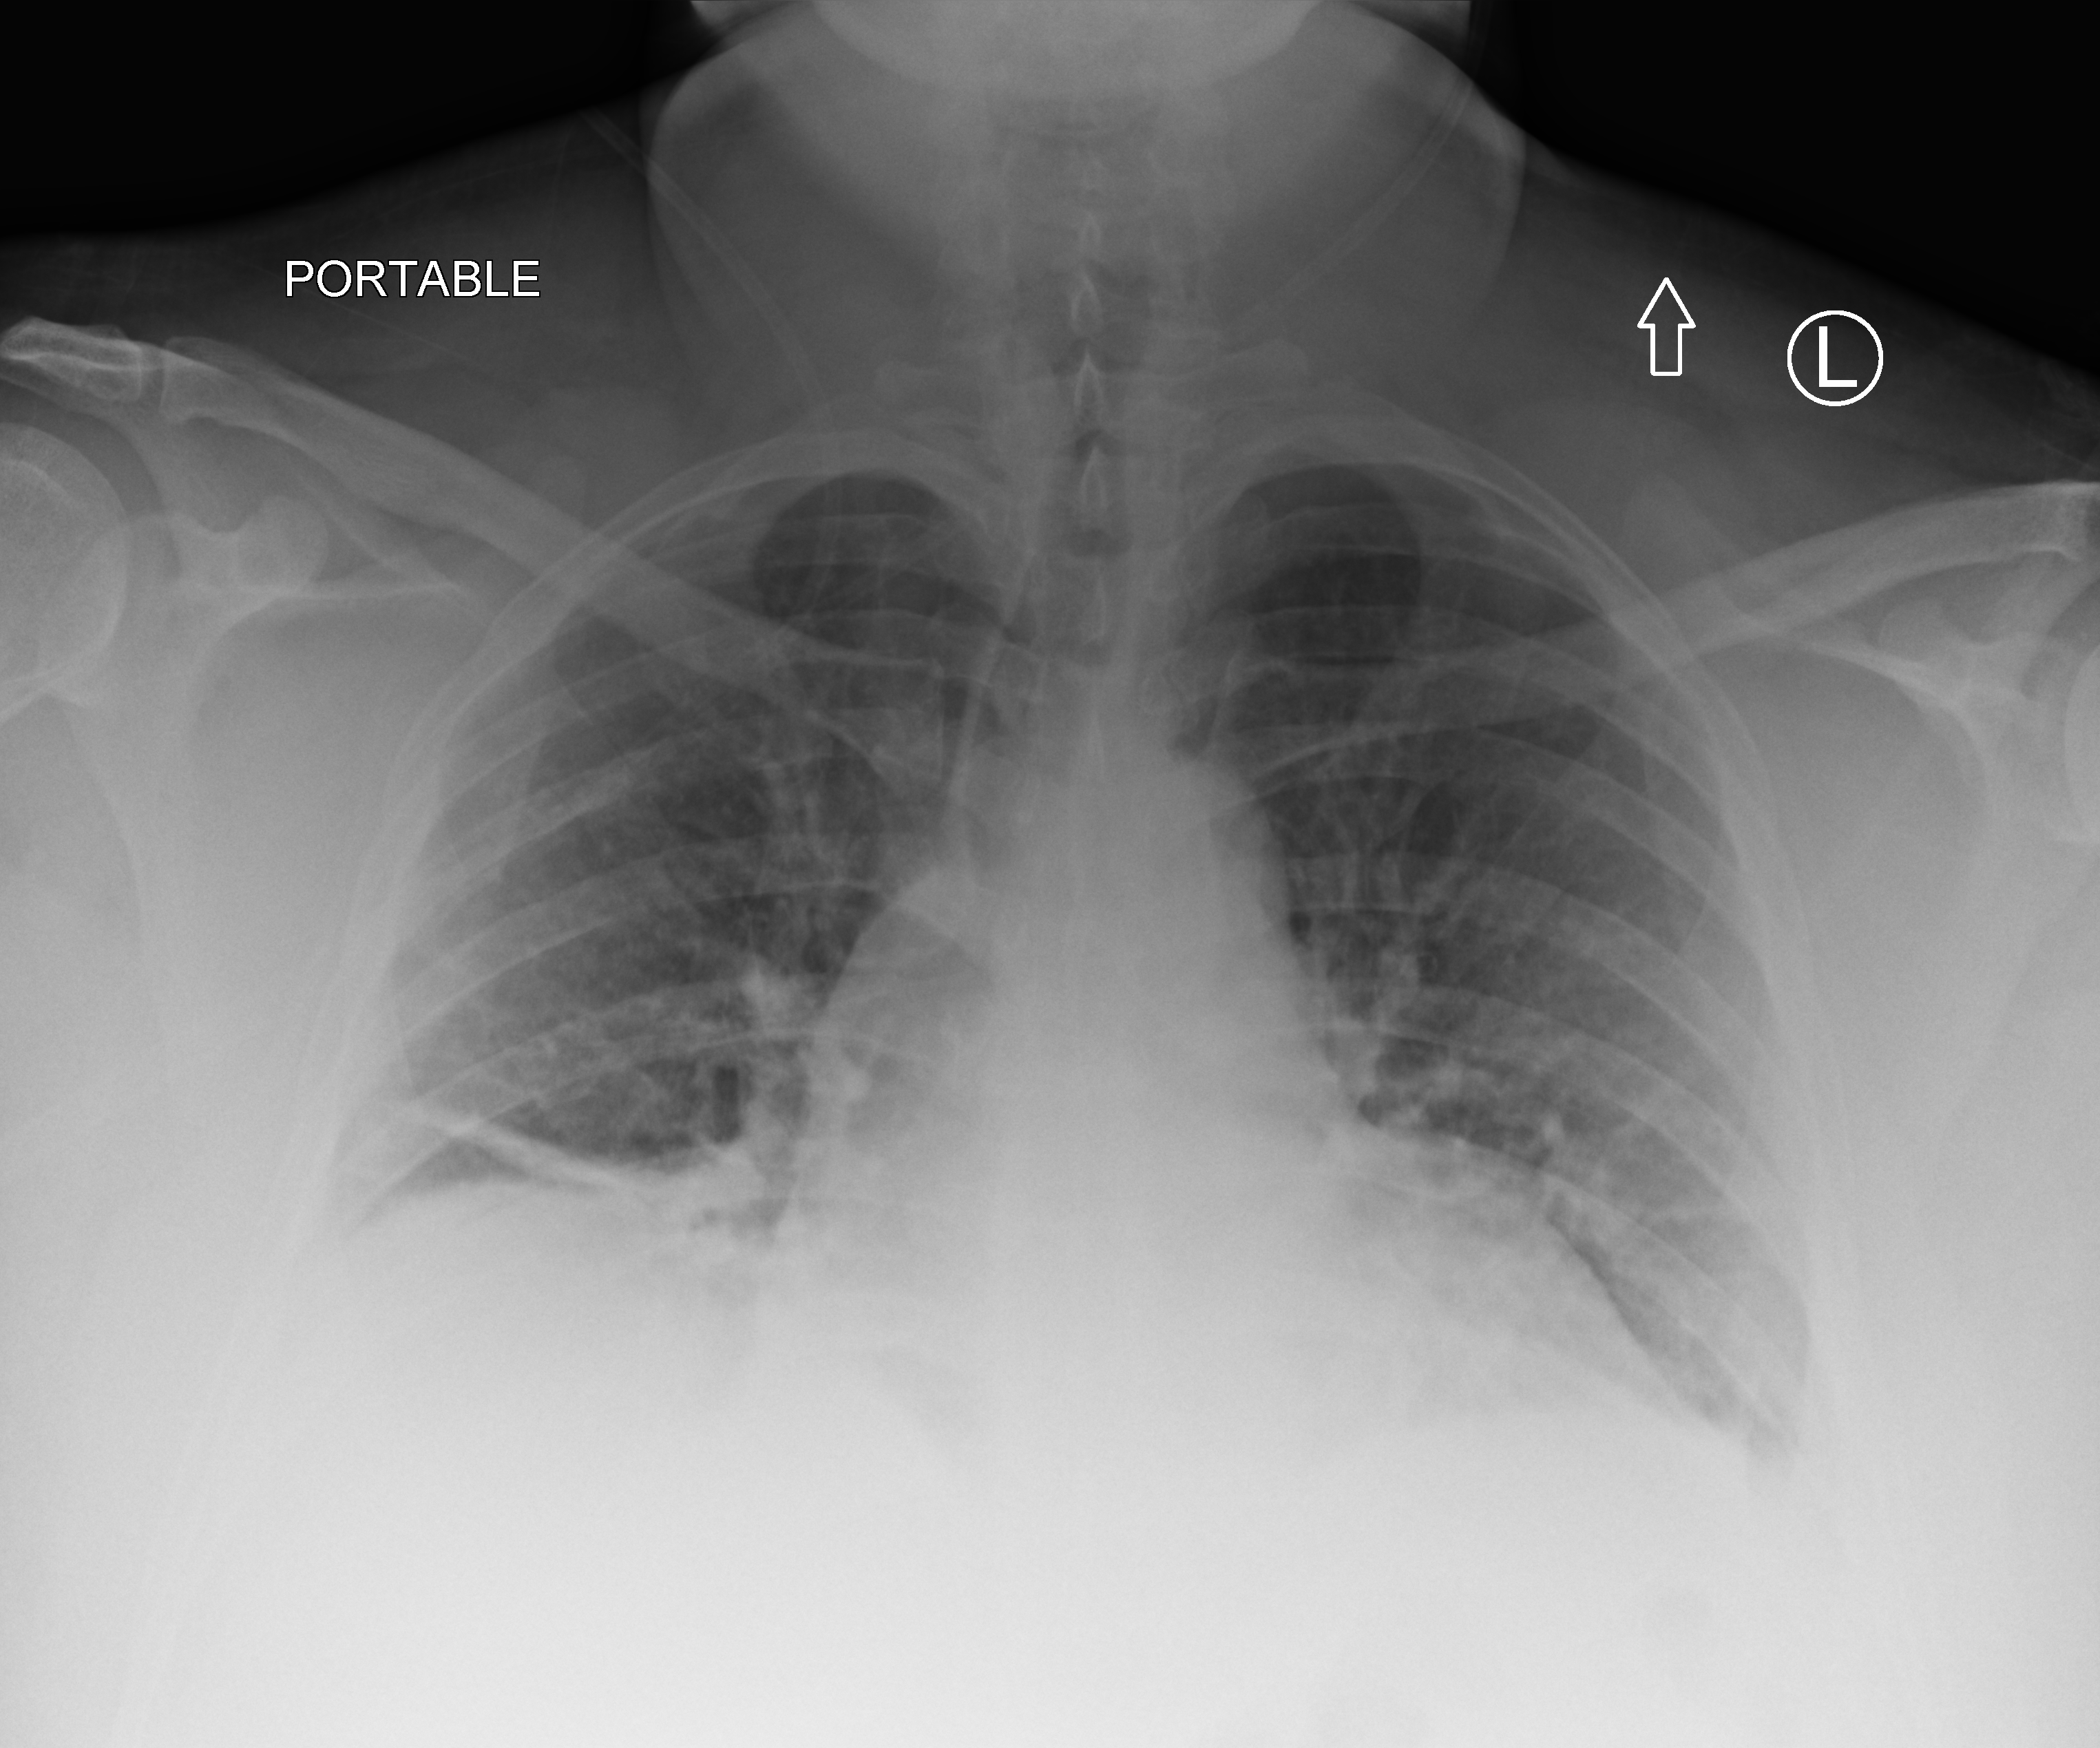
Portable chest radiograph; anteroposterior (AP) projection. Adult patient hospitalised with COVID-19, age 18–59 years.
Hospital-stay facts (about this admission, not read from this image; timing relative to this image not recorded): mechanically ventilated during this hospital stay: yes; admitted to intensive care during this hospital stay: yes.